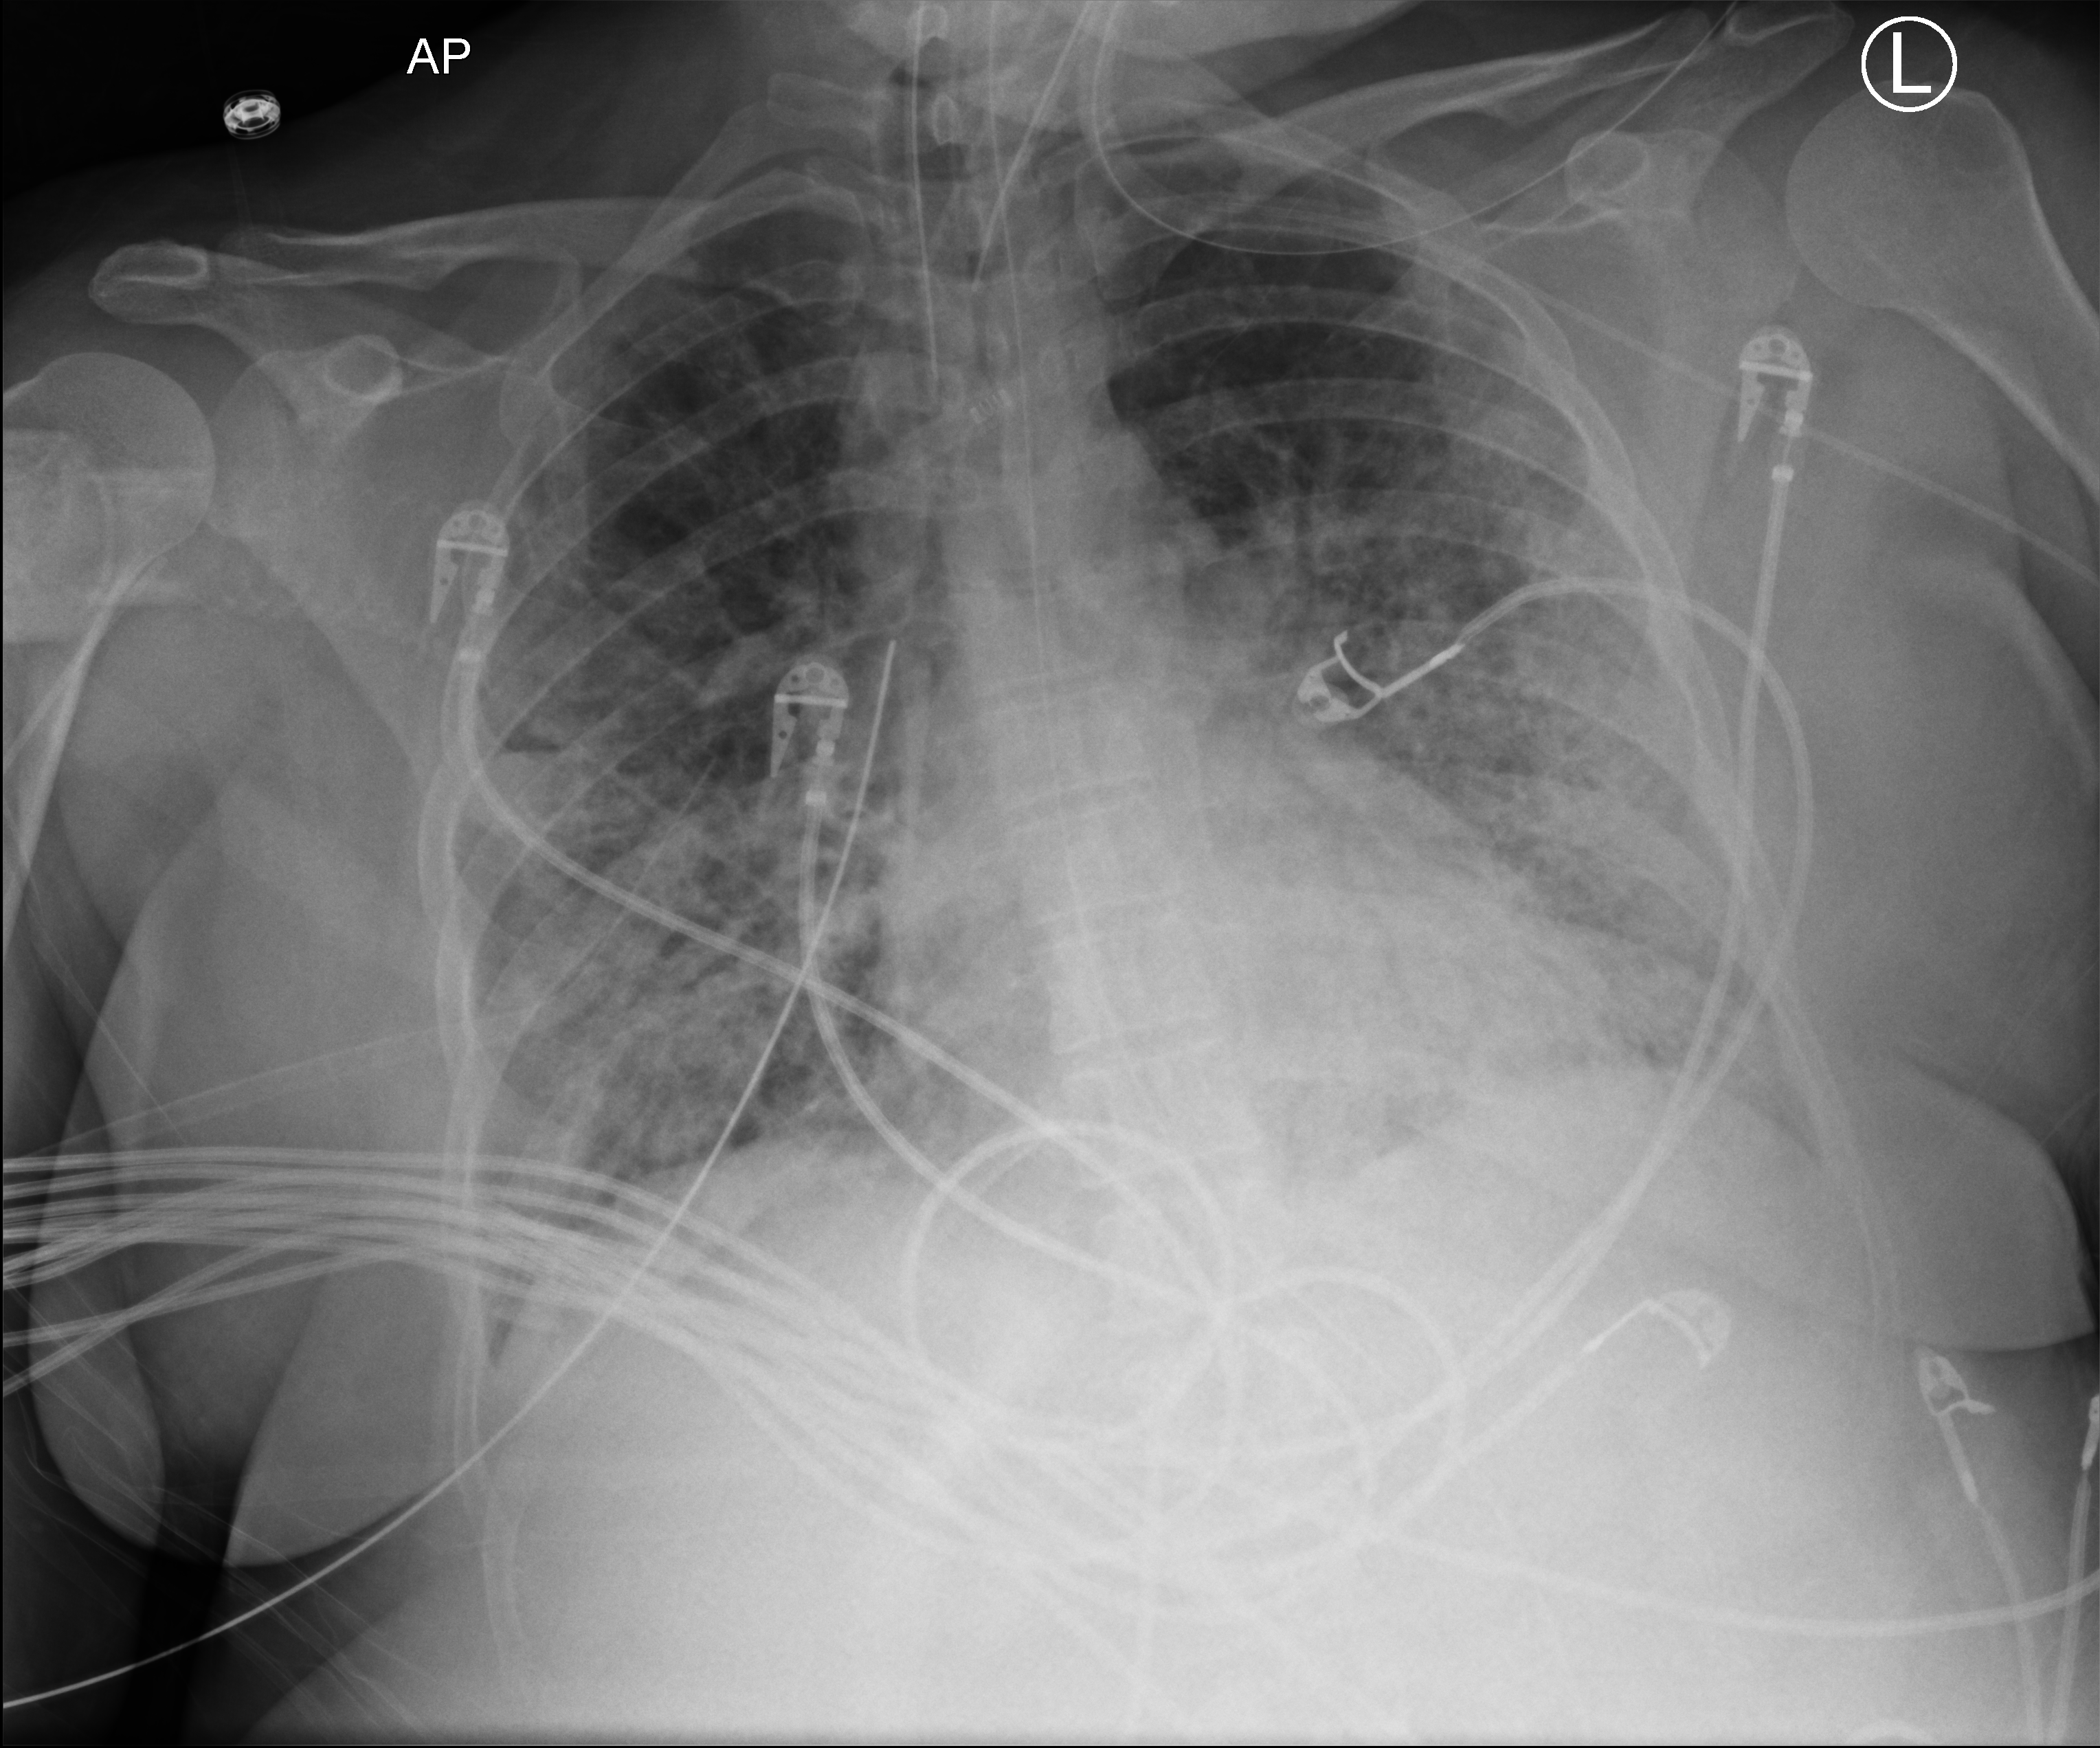
Bedside chest radiograph (computed radiography); anteroposterior (AP) projection. Female patient hospitalised with COVID-19, age 18–59 years.
Hospital-stay facts (about this admission, not read from this image; timing relative to this image not recorded):
- admitted to intensive care during this hospital stay: yes